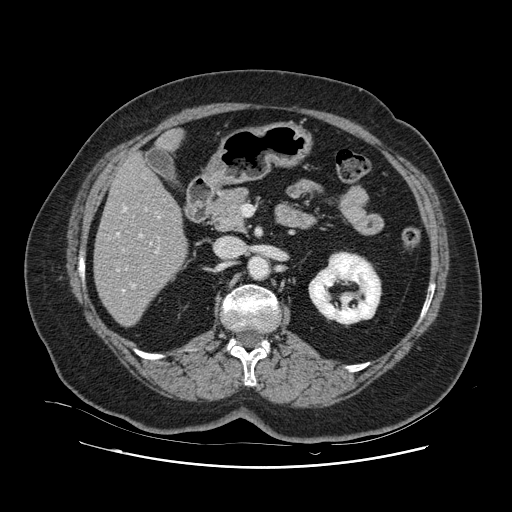
Contrast-enhanced abdominal CT, one axial slice. Position 44 of 132 along the scan axis. Intravenous contrast given. Soft-tissue window (W 400 / L 40 HU). 512 × 512 image matrix. Female patient, age 73 years. Case-level facts recorded for this patient, not image findings: diagnosis: colorectal cancer liver metastases, imaged before liver resection; multiple liver metastases: no; largest metastasis: 7 cm.
Structures marked on this image (manually delineated by an expert):
- hepatic veins: bounding box [x1, y1, x2, y2] px = [116, 207, 159, 292]
- liver: [95, 133, 186, 325]
- planned liver remnant (the part of the liver to remain after resection): [95, 157, 186, 325]
- portal vein (with intrahepatic branches): [132, 216, 160, 287]